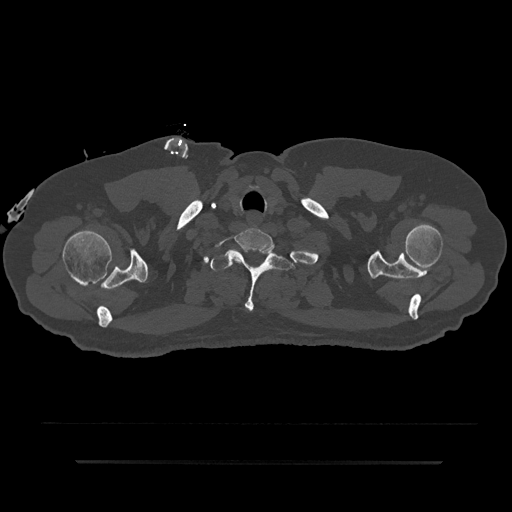
CT including the spine, one axial slice; position 750 of 797 along the scan axis; reconstruction kernel Br40s/3; 120 kVp; bone window (W 1800 / L 400 HU); 512 × 512 image matrix, field of view 464 × 464 mm. Male patient, age 59 years. Case-level facts recorded for this patient, not image findings: primary cancer: bile ducts; vertebrae with lytic lesions (as recorded): T10.
Annotated regions visible in this slice (semi-automatically segmented with operator editing):
- T1 vertebra: bounding box (x1, y1, x2, y2) in pixels: (210, 248, 293, 312)